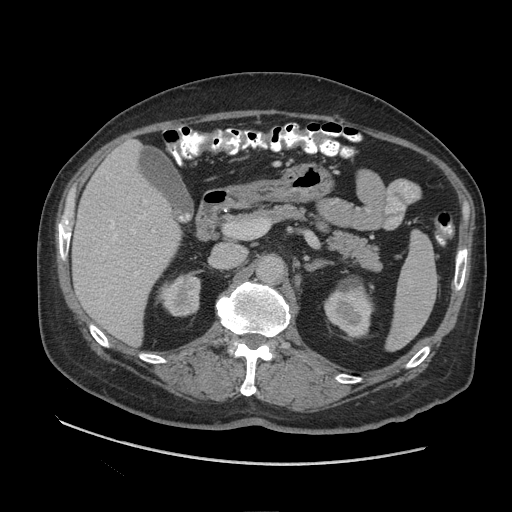
Contrast-enhanced abdominal CT (liver protocol), one axial slice; slice 48 of 109 in the series (ordered by position); reconstruction kernel STANDARD; soft-tissue window (W 400 / L 40 HU); 2.5 mm slice thickness; 512 × 512 image matrix, field of view 420 × 420 mm. Case-level facts recorded for this patient, not image findings: diagnosis: hepatocellular carcinoma (patient treated with transarterial chemoembolisation; whether this scan precedes or follows treatment is not stated here); TNM stage (as recorded): Stage-I; Child-Pugh class: A.
Annotated regions visible in this slice (semi-automatic segmentation, software-assisted and operator-edited):
- liver parenchyma outside the tumour (the mass and vessels are separate outlines, so this box may not span the whole liver): bounding box <72,140,180,344> (left, top, right, bottom; pixels)
- liver vessels: <96,178,154,276>